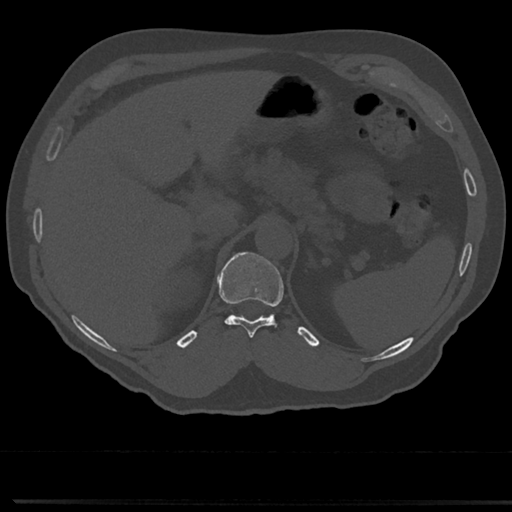
CT including the spine, one axial slice; slice 196 of 817 in the series (ordered by position); 120 kVp; bone window (W 1800 / L 400 HU); 512 × 512 image matrix, field of view 355 × 355 mm. Male patient, age 61 years. Case-level facts recorded for this patient, not image findings: primary cancer: prostate.
Structures marked on this image (semi-automatic segmentation, software-assisted and operator-edited):
- T11 vertebra: bounding box (x1, y1, x2, y2) in pixels: (219, 253, 284, 339)
- T12 vertebra: (218, 252, 255, 278)